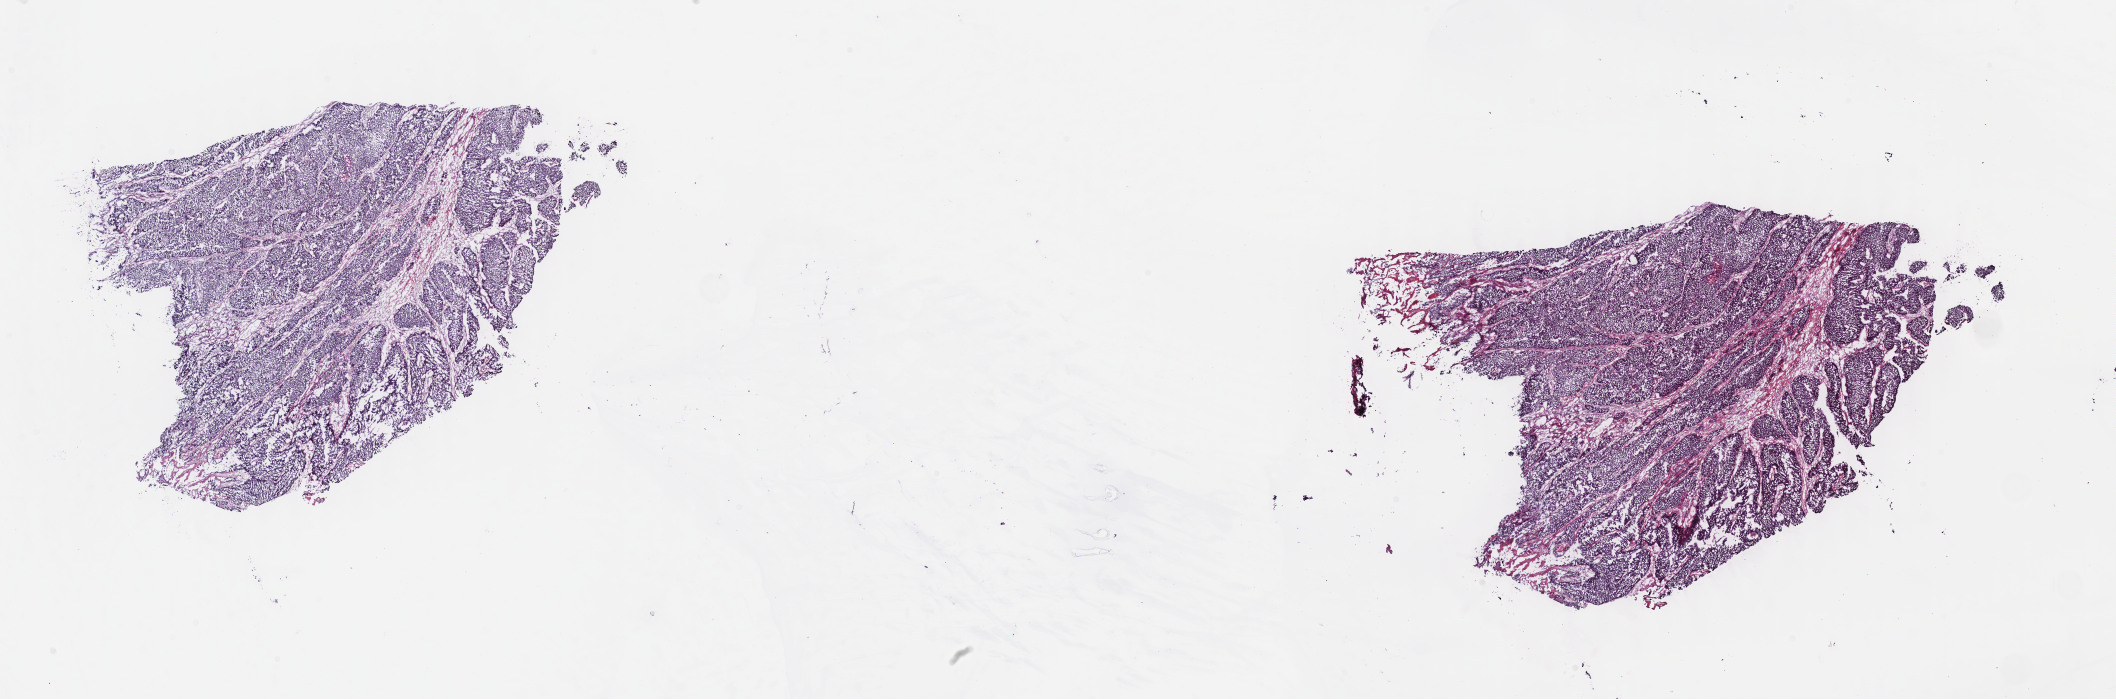
H&E whole-slide image — a low-resolution overview of the entire scanned area, about 34.2 x 11.3 mm (slide scanned at 40x); frozen section from the top of the tissue portion; bladder, primary tumour sample. Patient: female, age at initial diagnosis 55 years. Histologic grade: high grade. Pathologist review of this section (percent, as recorded): tumour cells 75%, tumour nuclei 92%, normal cells 0%, stromal cells 23%, necrosis 2%. Infiltration values recorded for this section: lymphocyte infiltration 3%, monocyte infiltration 0%, neutrophil infiltration 1%.
AJCC pathologic stage: II (6th edition). Pathologic diagnosis: Transitional cell carcinoma.